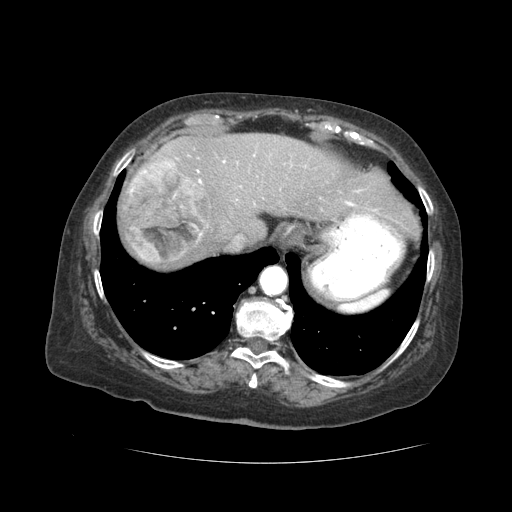
Contrast-enhanced abdominal CT (liver protocol), one axial slice; slice 38 of 59 in the series (ordered by position); reconstruction kernel STANDARD; 120 kVp; soft-tissue window (W 400 / L 40 HU); 512 × 512 image matrix, field of view 380 × 380 mm. From the clinical record (not read from this slice): diagnosis: hepatocellular carcinoma (patient treated with transarterial chemoembolisation; whether this scan precedes or follows treatment is not stated here); TNM stage (as recorded): Stage-I; Child-Pugh class: A; tumour nodularity: uninodular.
Annotated regions visible in this slice (semi-automatic segmentation, software-assisted and operator-edited):
- liver parenchyma outside the tumour (the mass and vessels are separate outlines, so this box may not span the whole liver): bounding box [x1, y1, x2, y2] px = [120, 134, 416, 264]
- mass: [123, 157, 211, 262]
- liver vessels: [176, 154, 376, 211]